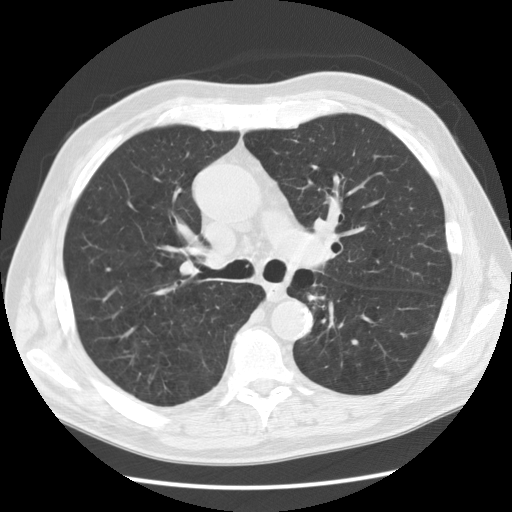
Axial slice from a low-dose chest CT screening exam. Second annual screen. Lung window (W 1500 / L -600 HU). Standard (soft-tissue) reconstruction kernel (STANDARD). Slice 49 of 130 in the series. 512 × 512 image matrix, field of view 362 × 362 mm. Male participant, aged 73 years at enrolment. Current smoker at enrolment.
Expert-annotated lung lesion, box from (x=292, y=275) to (x=338, y=318) px. The screening reader recorded 4 non-calcified nodules or masses ≥4 mm on this exam (right upper lobe, right upper lobe, left upper lobe, right lower lobe); which of them this box marks is not recorded. Official screen result: positive, no significant change: stable abnormalities potentially related to lung cancer, unchanged since the prior screening exam. Later outcome: lung cancer diagnosed 302 days after this screen — small cell carcinoma, NOS, left lower lobe, stage IIIB (AJCC 6th edition), 55 mm at pathology.